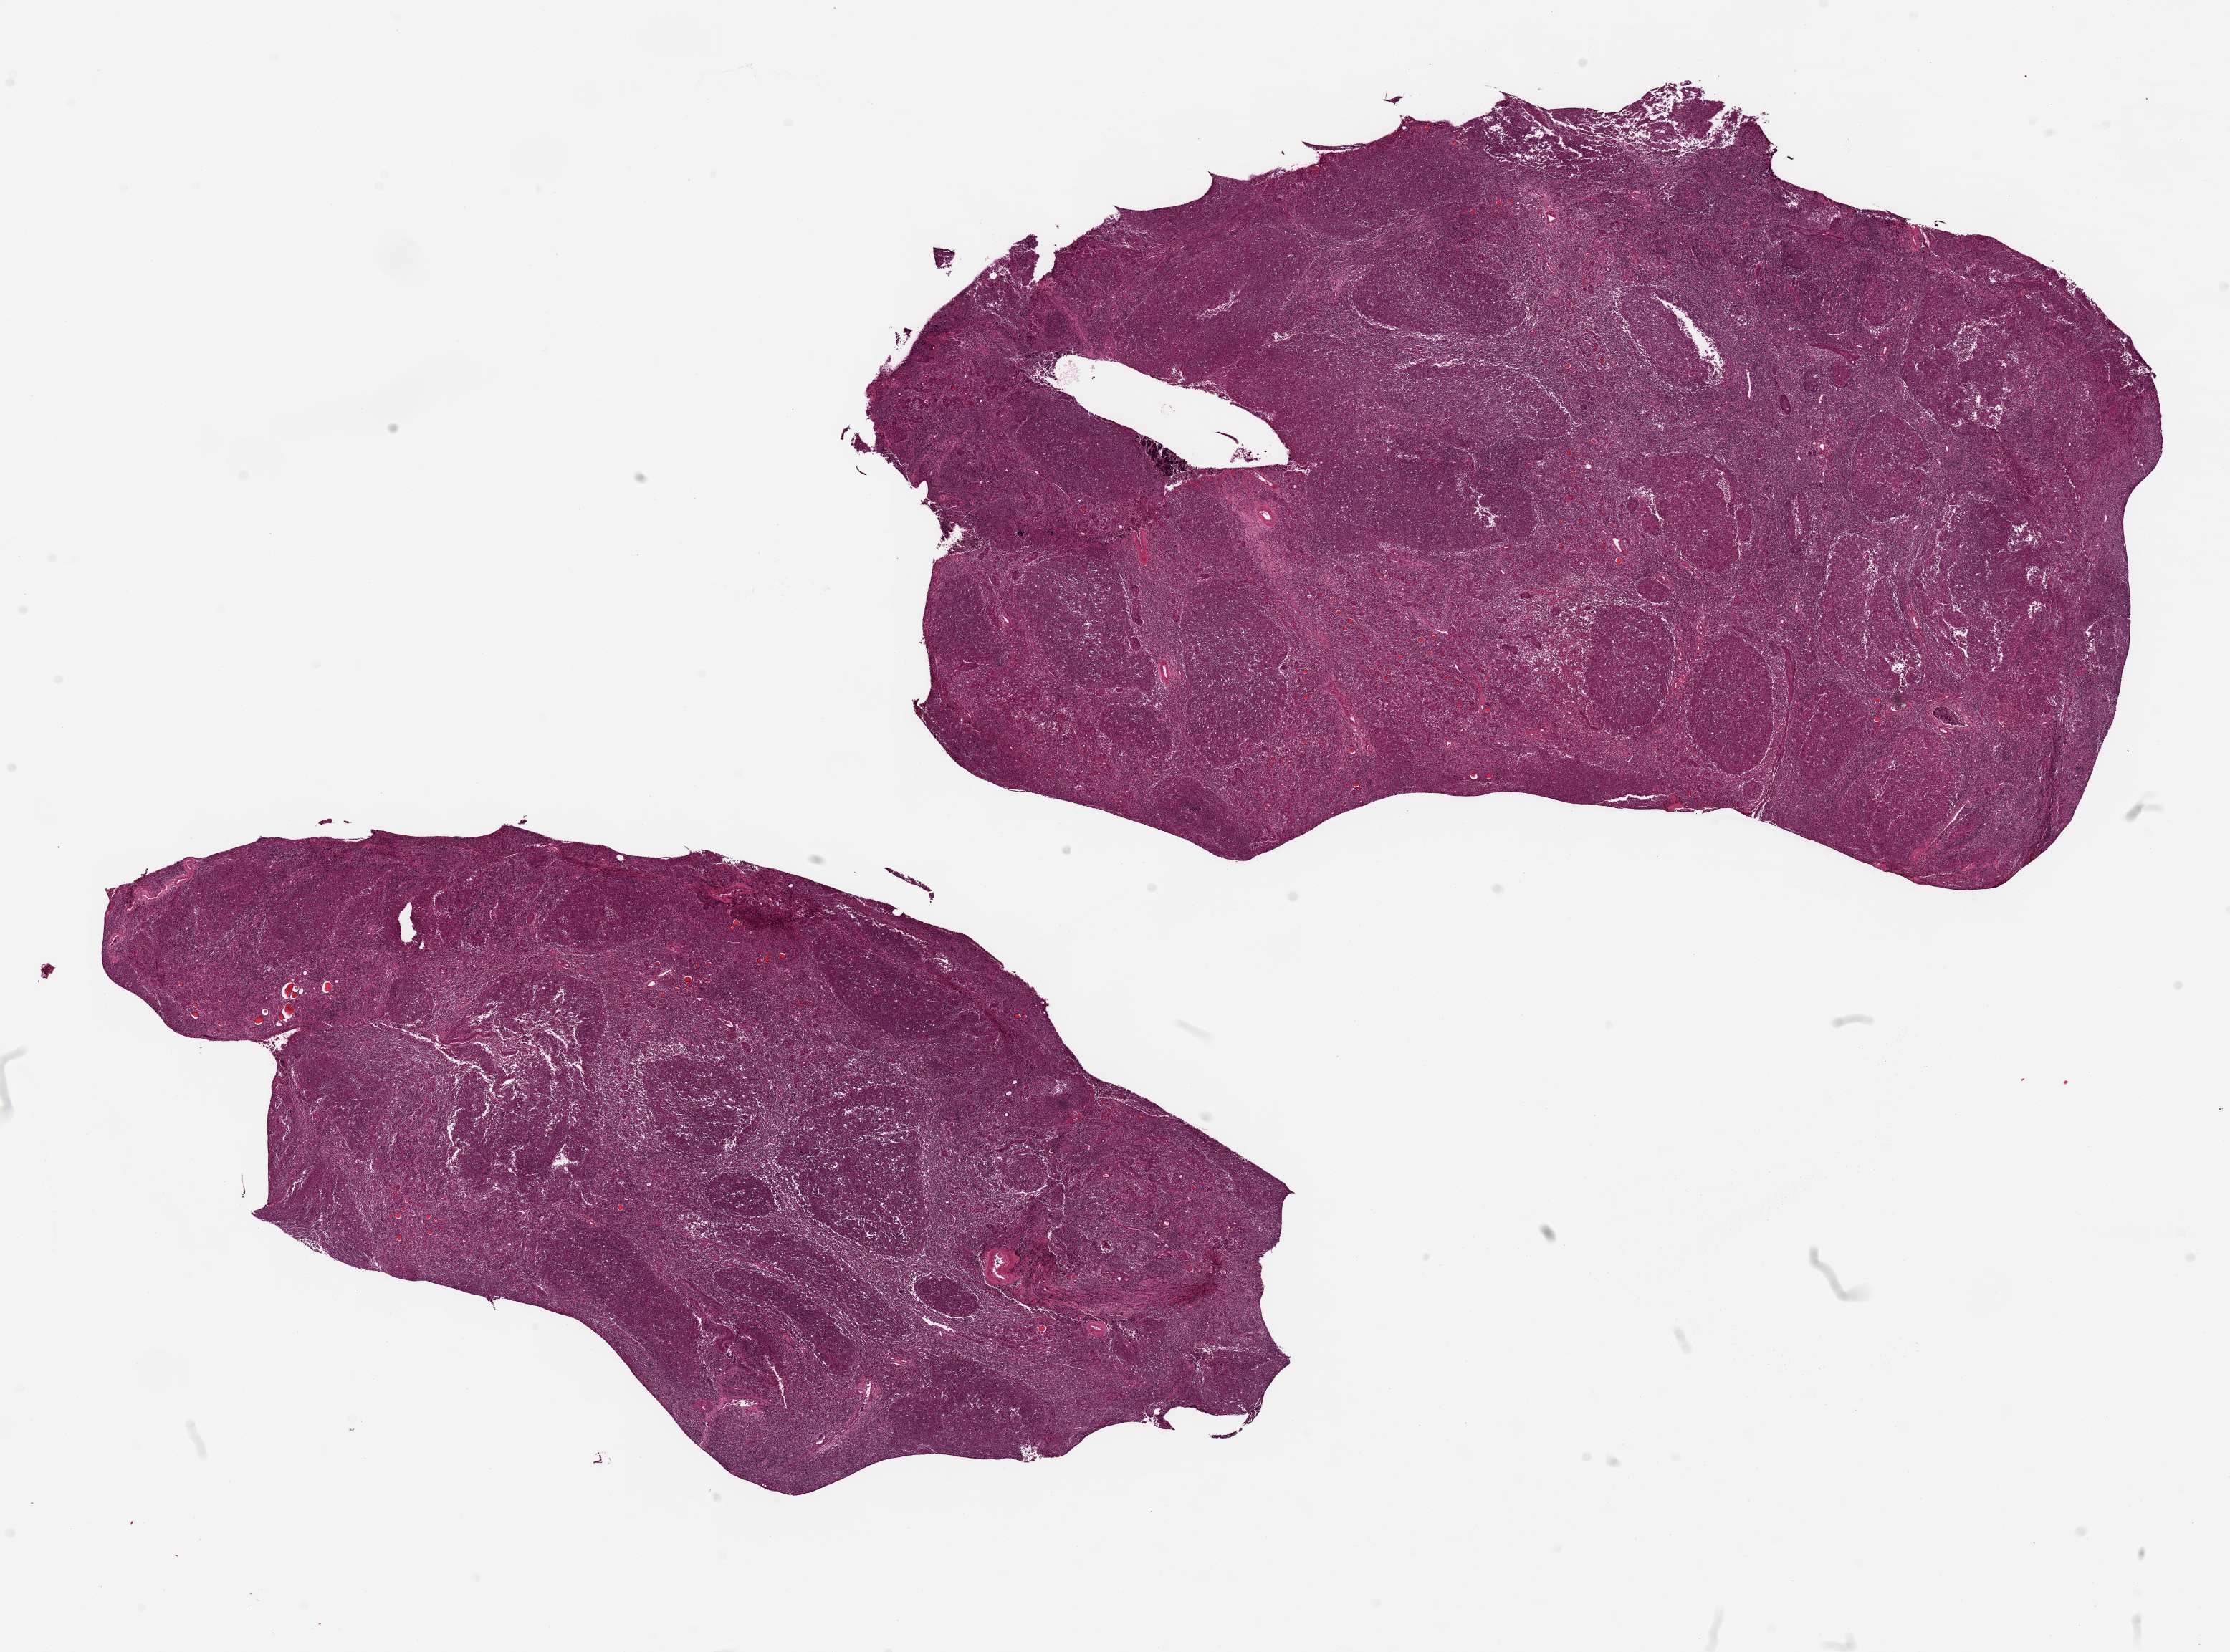
Whole-slide image, H&E stain — low-resolution overview of the scanned area, about 24.6 x 18.2 mm; PAXgene-fixed, paraffin-embedded tissue; section of thyroid (target tissue); tissue donor sample. Donor: male.
Review note (as recorded): 2 pieces 14x7 & 14x^ mm; severe Hashimoto's thyroiditis.